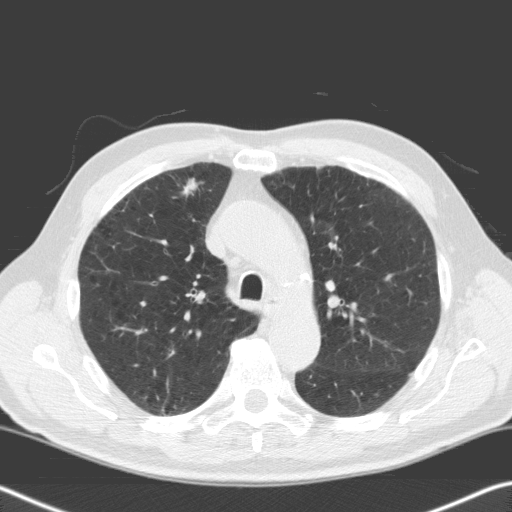
Axial slice from a low-dose chest CT screening exam, baseline screening round, lung window (W 1500 / L -600 HU), 3.2 mm slice thickness, standard (soft-tissue) reconstruction kernel (C), slice 47 of 170 in the series. Male participant, aged 68 years at enrolment. Current smoker at enrolment.
Expert reader's lesion annotation, bounding box [x1, y1, x2, y2] px = [161, 168, 210, 216]. The exam's reader record, not a measurement of the box and not confirmed to be the same lesion: non-calcified nodule or mass ≥4 mm, right upper lobe, 18 × 12 mm, spiculated (stellate) margins, soft tissue attenuation. Official screen result: positive, change unspecified: nodule(s) >= 4 mm or enlarging nodule(s), mass(es), or other non-specific abnormalities suspicious for lung cancer. Later outcome: lung cancer diagnosed 73 days after this screen — squamous cell carcinoma, NOS, right upper lobe, moderately differentiated (G2), stage IIIA (AJCC 6th edition), 7 mm at pathology.